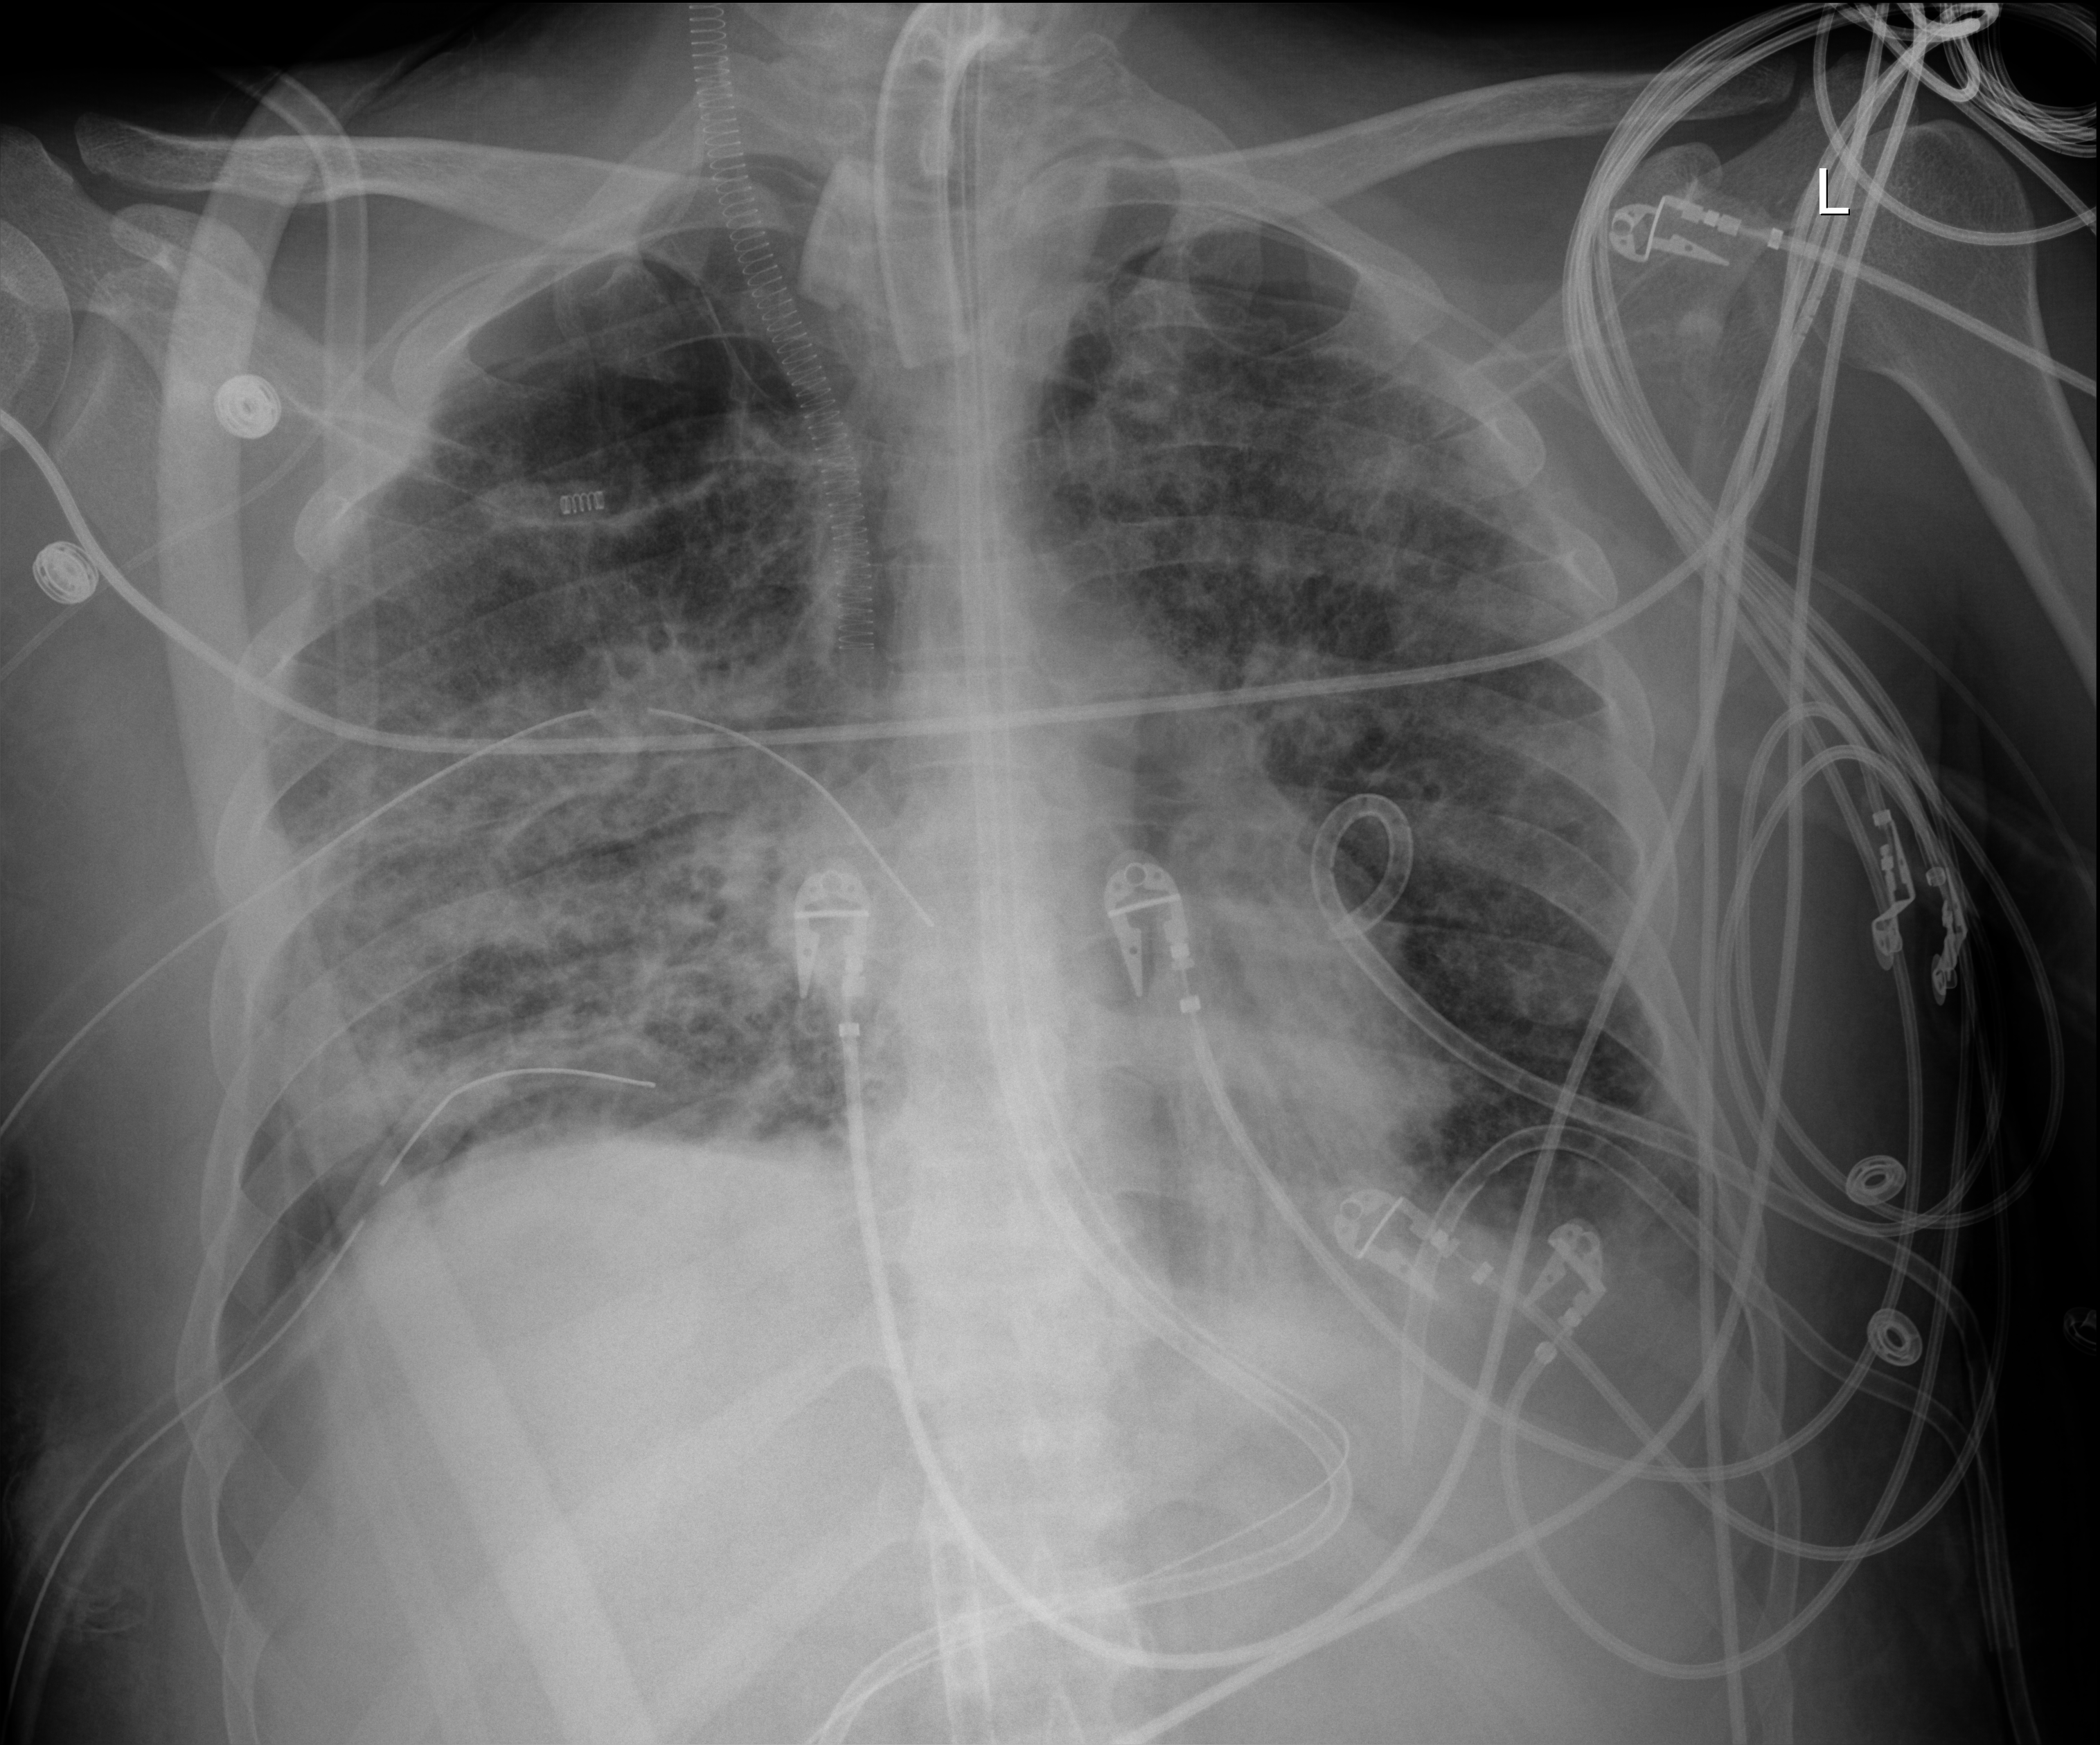
Bedside chest radiograph (digital radiography). Patient hospitalised with COVID-19, aged 18–59 years.
Hospital-stay facts (about this admission, not read from this image; timing relative to this image not recorded): diabetes (admission record): no.